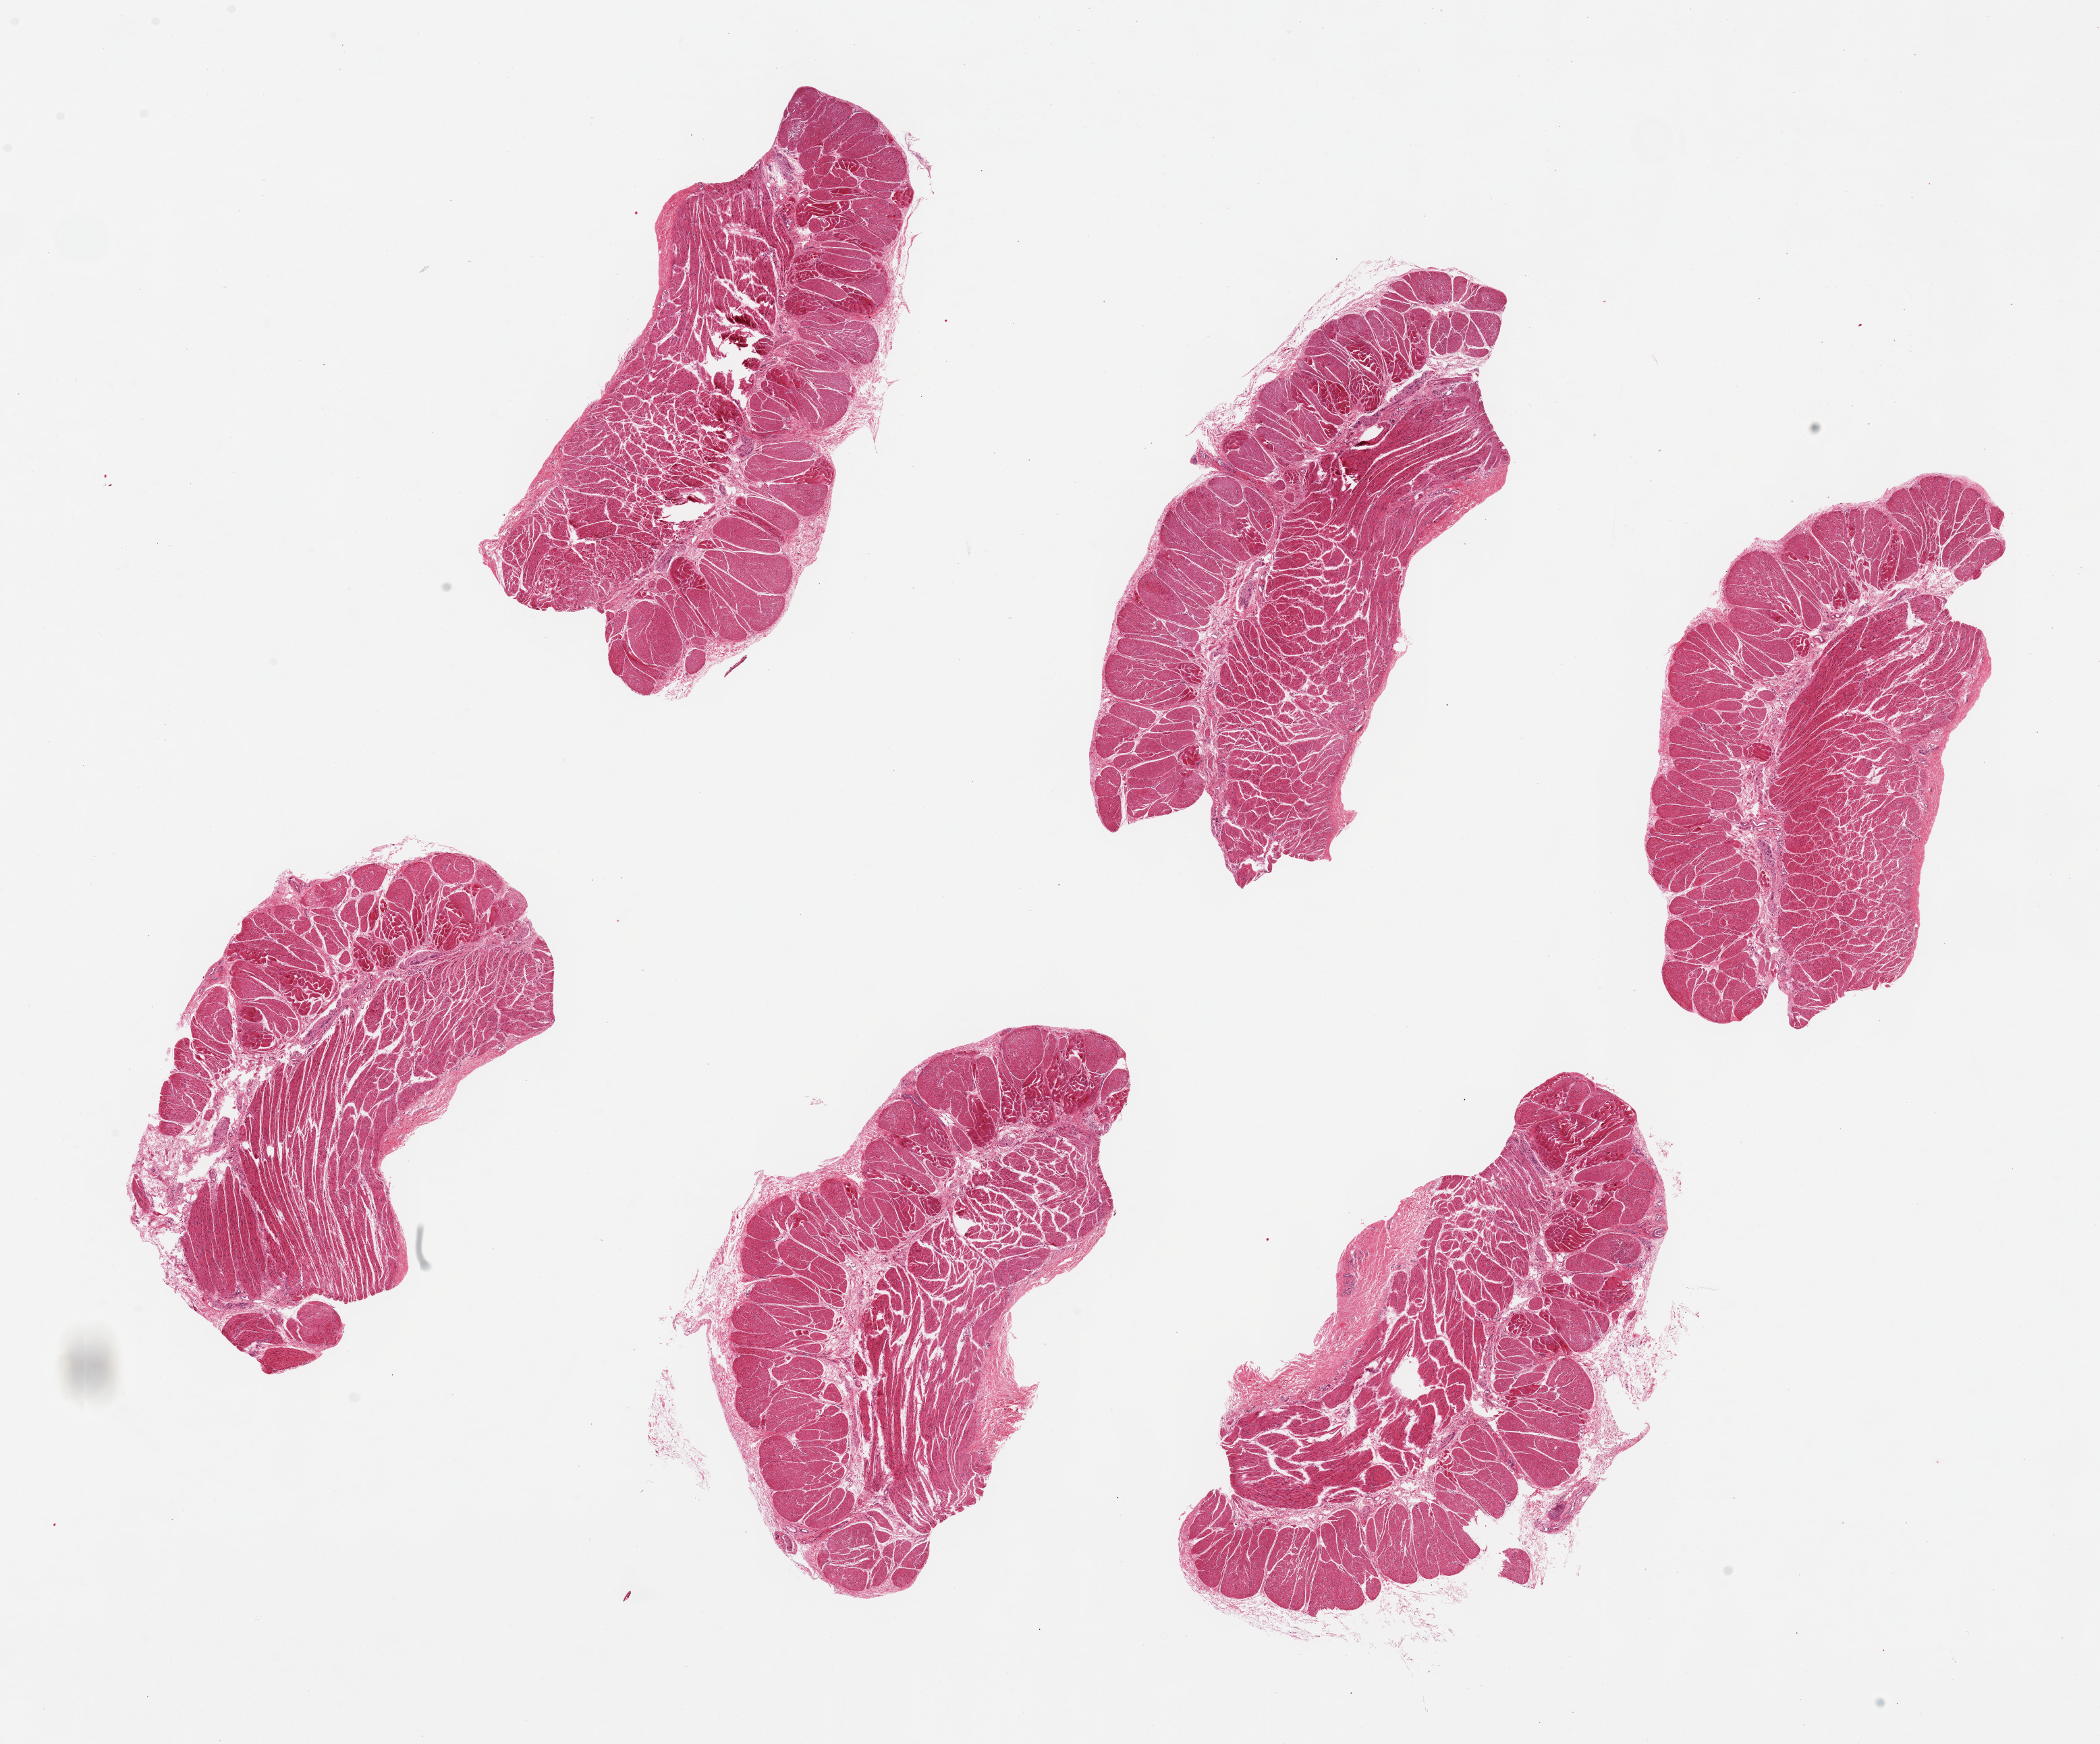
Haematoxylin and eosin whole-slide image, low-resolution overview of the scanned area, about 24.6 x 20.4 mm (slide scanned at 20x). PAXgene-fixed paraffin-embedded (PFPE) section. Section of esophageal muscle (target tissue). Donor tissue sample.
Pathologist's review note for this sample: 6 pieces up to 7x3 mm.